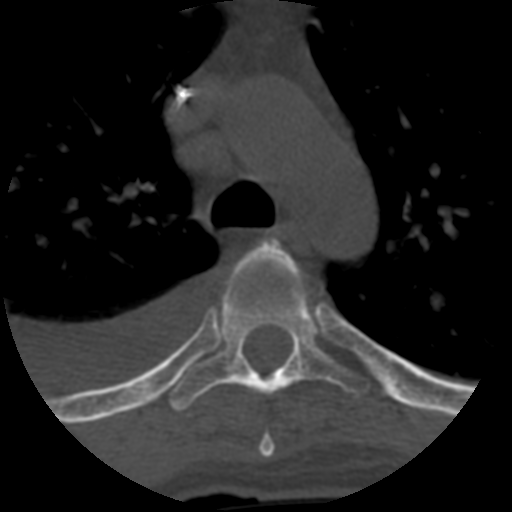
CT including the spine, one axial slice; position 459 of 708 along the scan axis; one of 3 acquisitions stored at this slice position; bone window (W 1800 / L 400 HU); 512 × 512 image matrix, field of view 160 × 160 mm. Patient age 55 years. From the clinical record (not read from this slice): primary cancer: colon; vertebrae with lytic lesions (as recorded): T12, L1, L5.
Outlined on this slice (semi-automatic segmentation, software-assisted and operator-edited):
- T4 vertebra: box from (x=222, y=236) to (x=306, y=458) px
- T5 vertebra: (x=169, y=290)–(x=369, y=412)